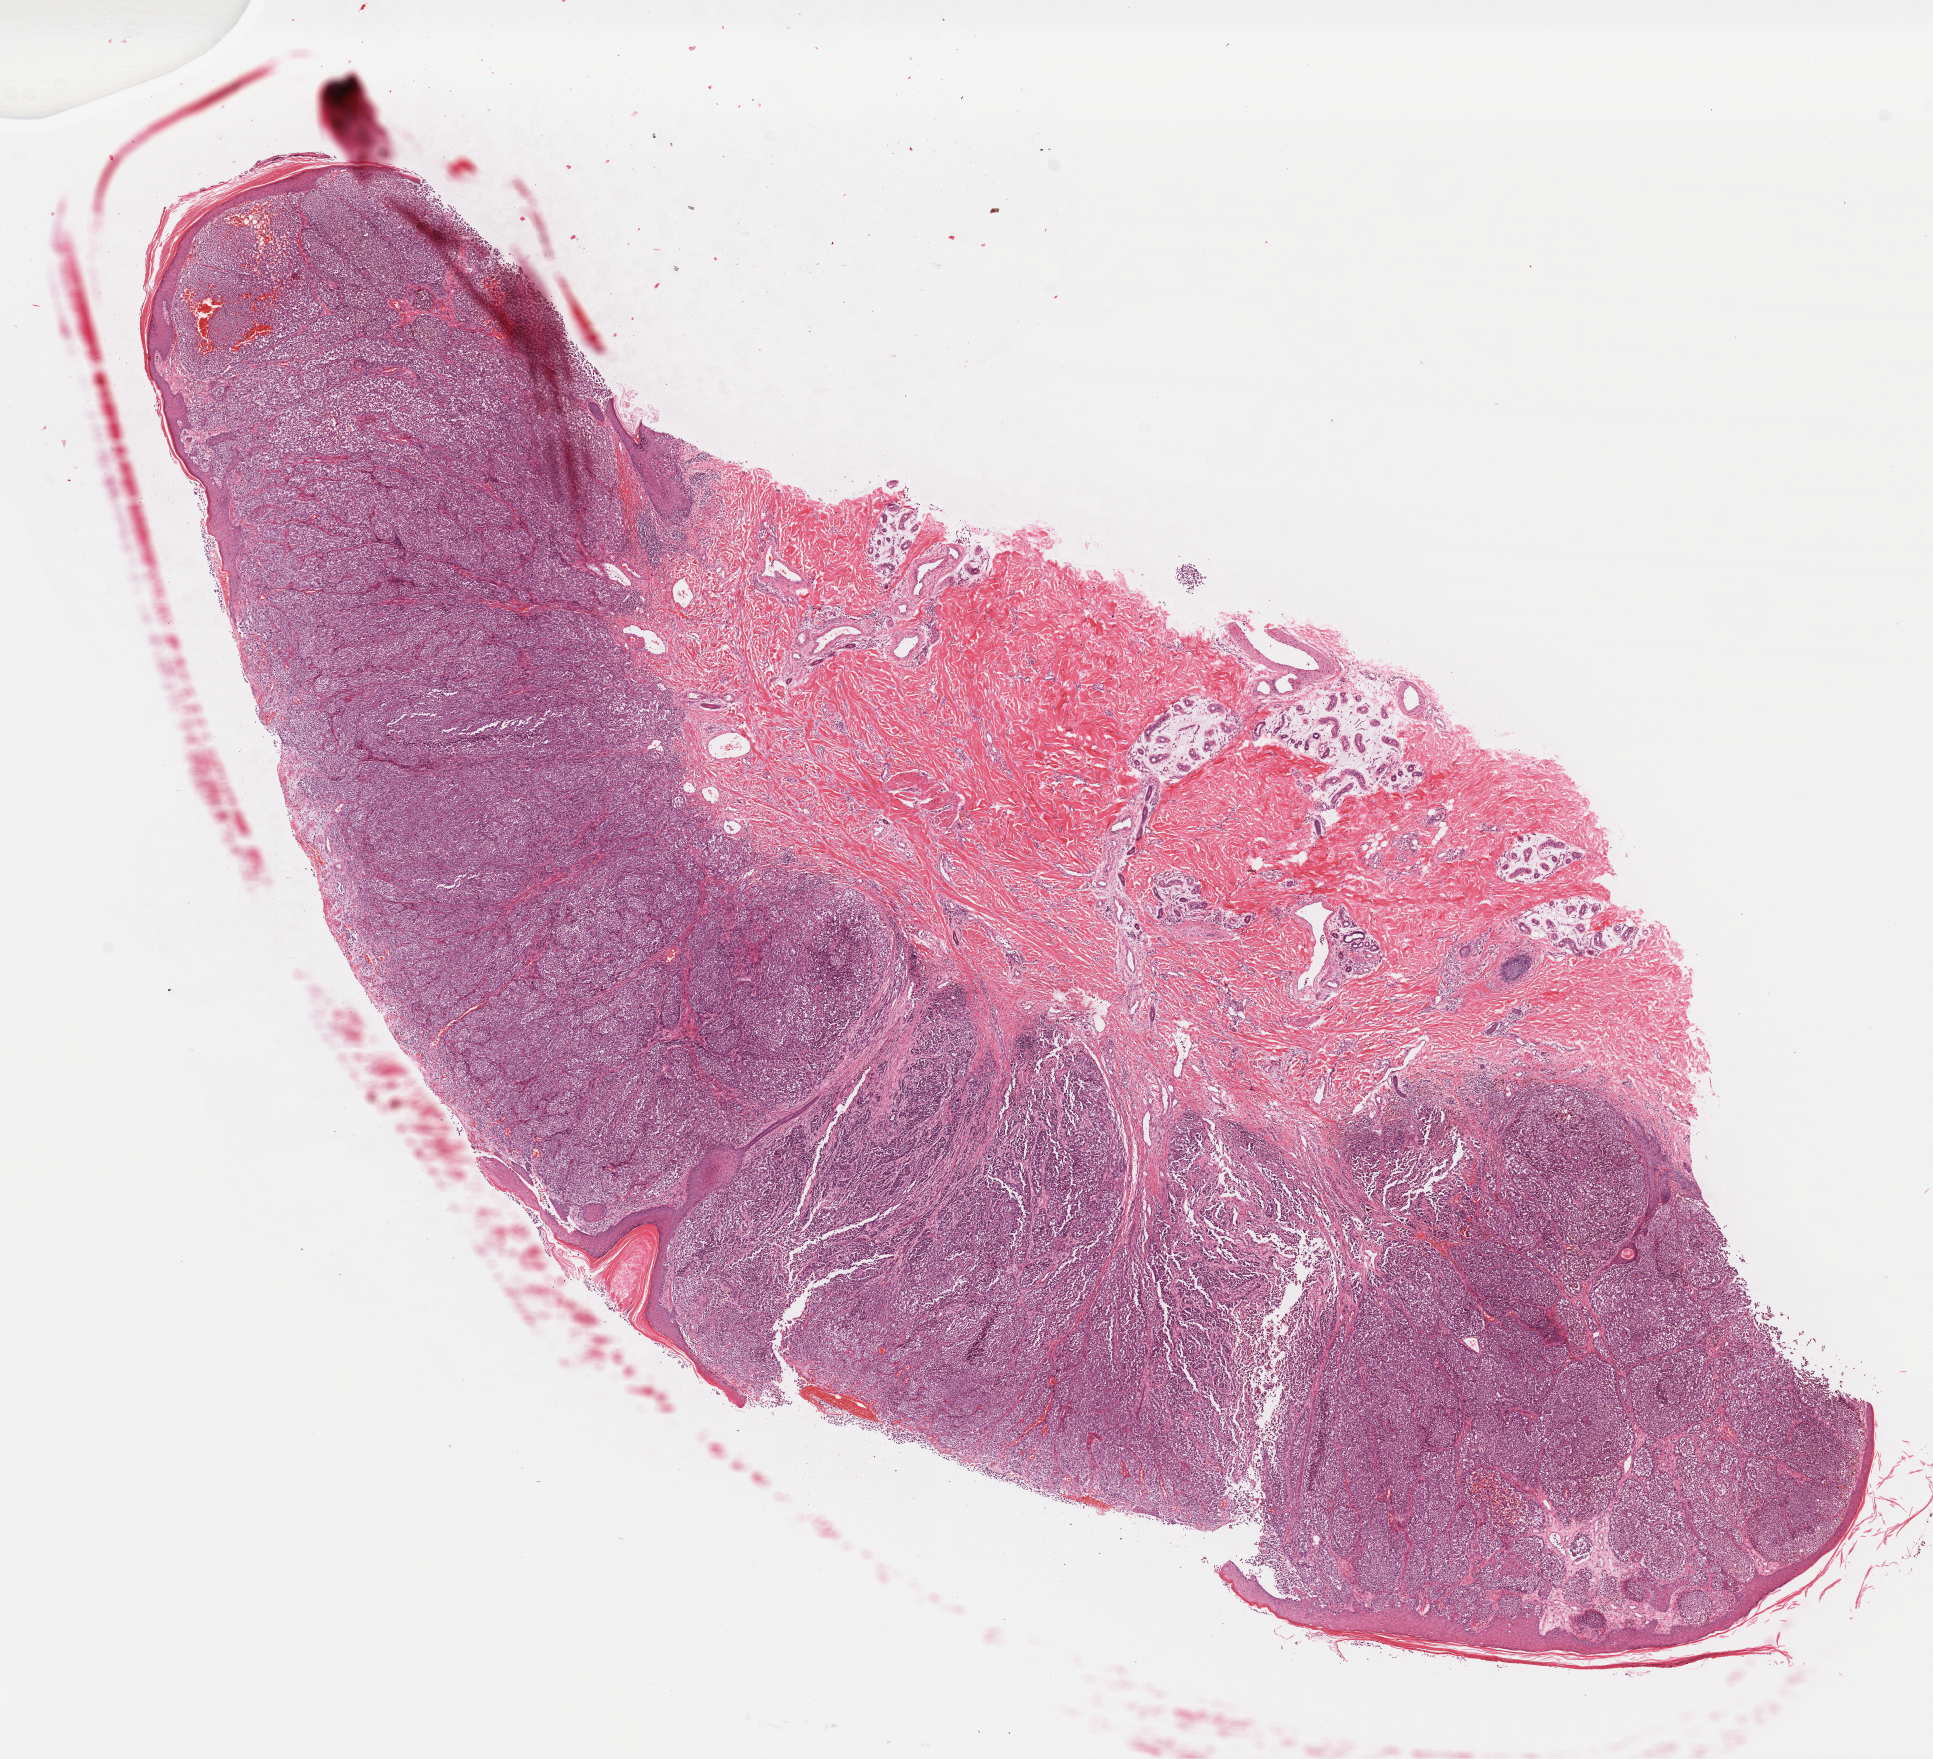
Digitized Hematoxylin and eosin (H&E) stained tissue section (whole slide), low-resolution overview of the scanned area, about 15.2 x 13.8 mm (acquisition: 40x scan). Formalin-fixed paraffin-embedded (FFPE) diagnostic section. Skin, primary tumour sample. Male patient; age at initial diagnosis 73 years.
- AJCC pathologic stage: IIB (7th edition)
- histologic diagnosis: Nodular melanoma